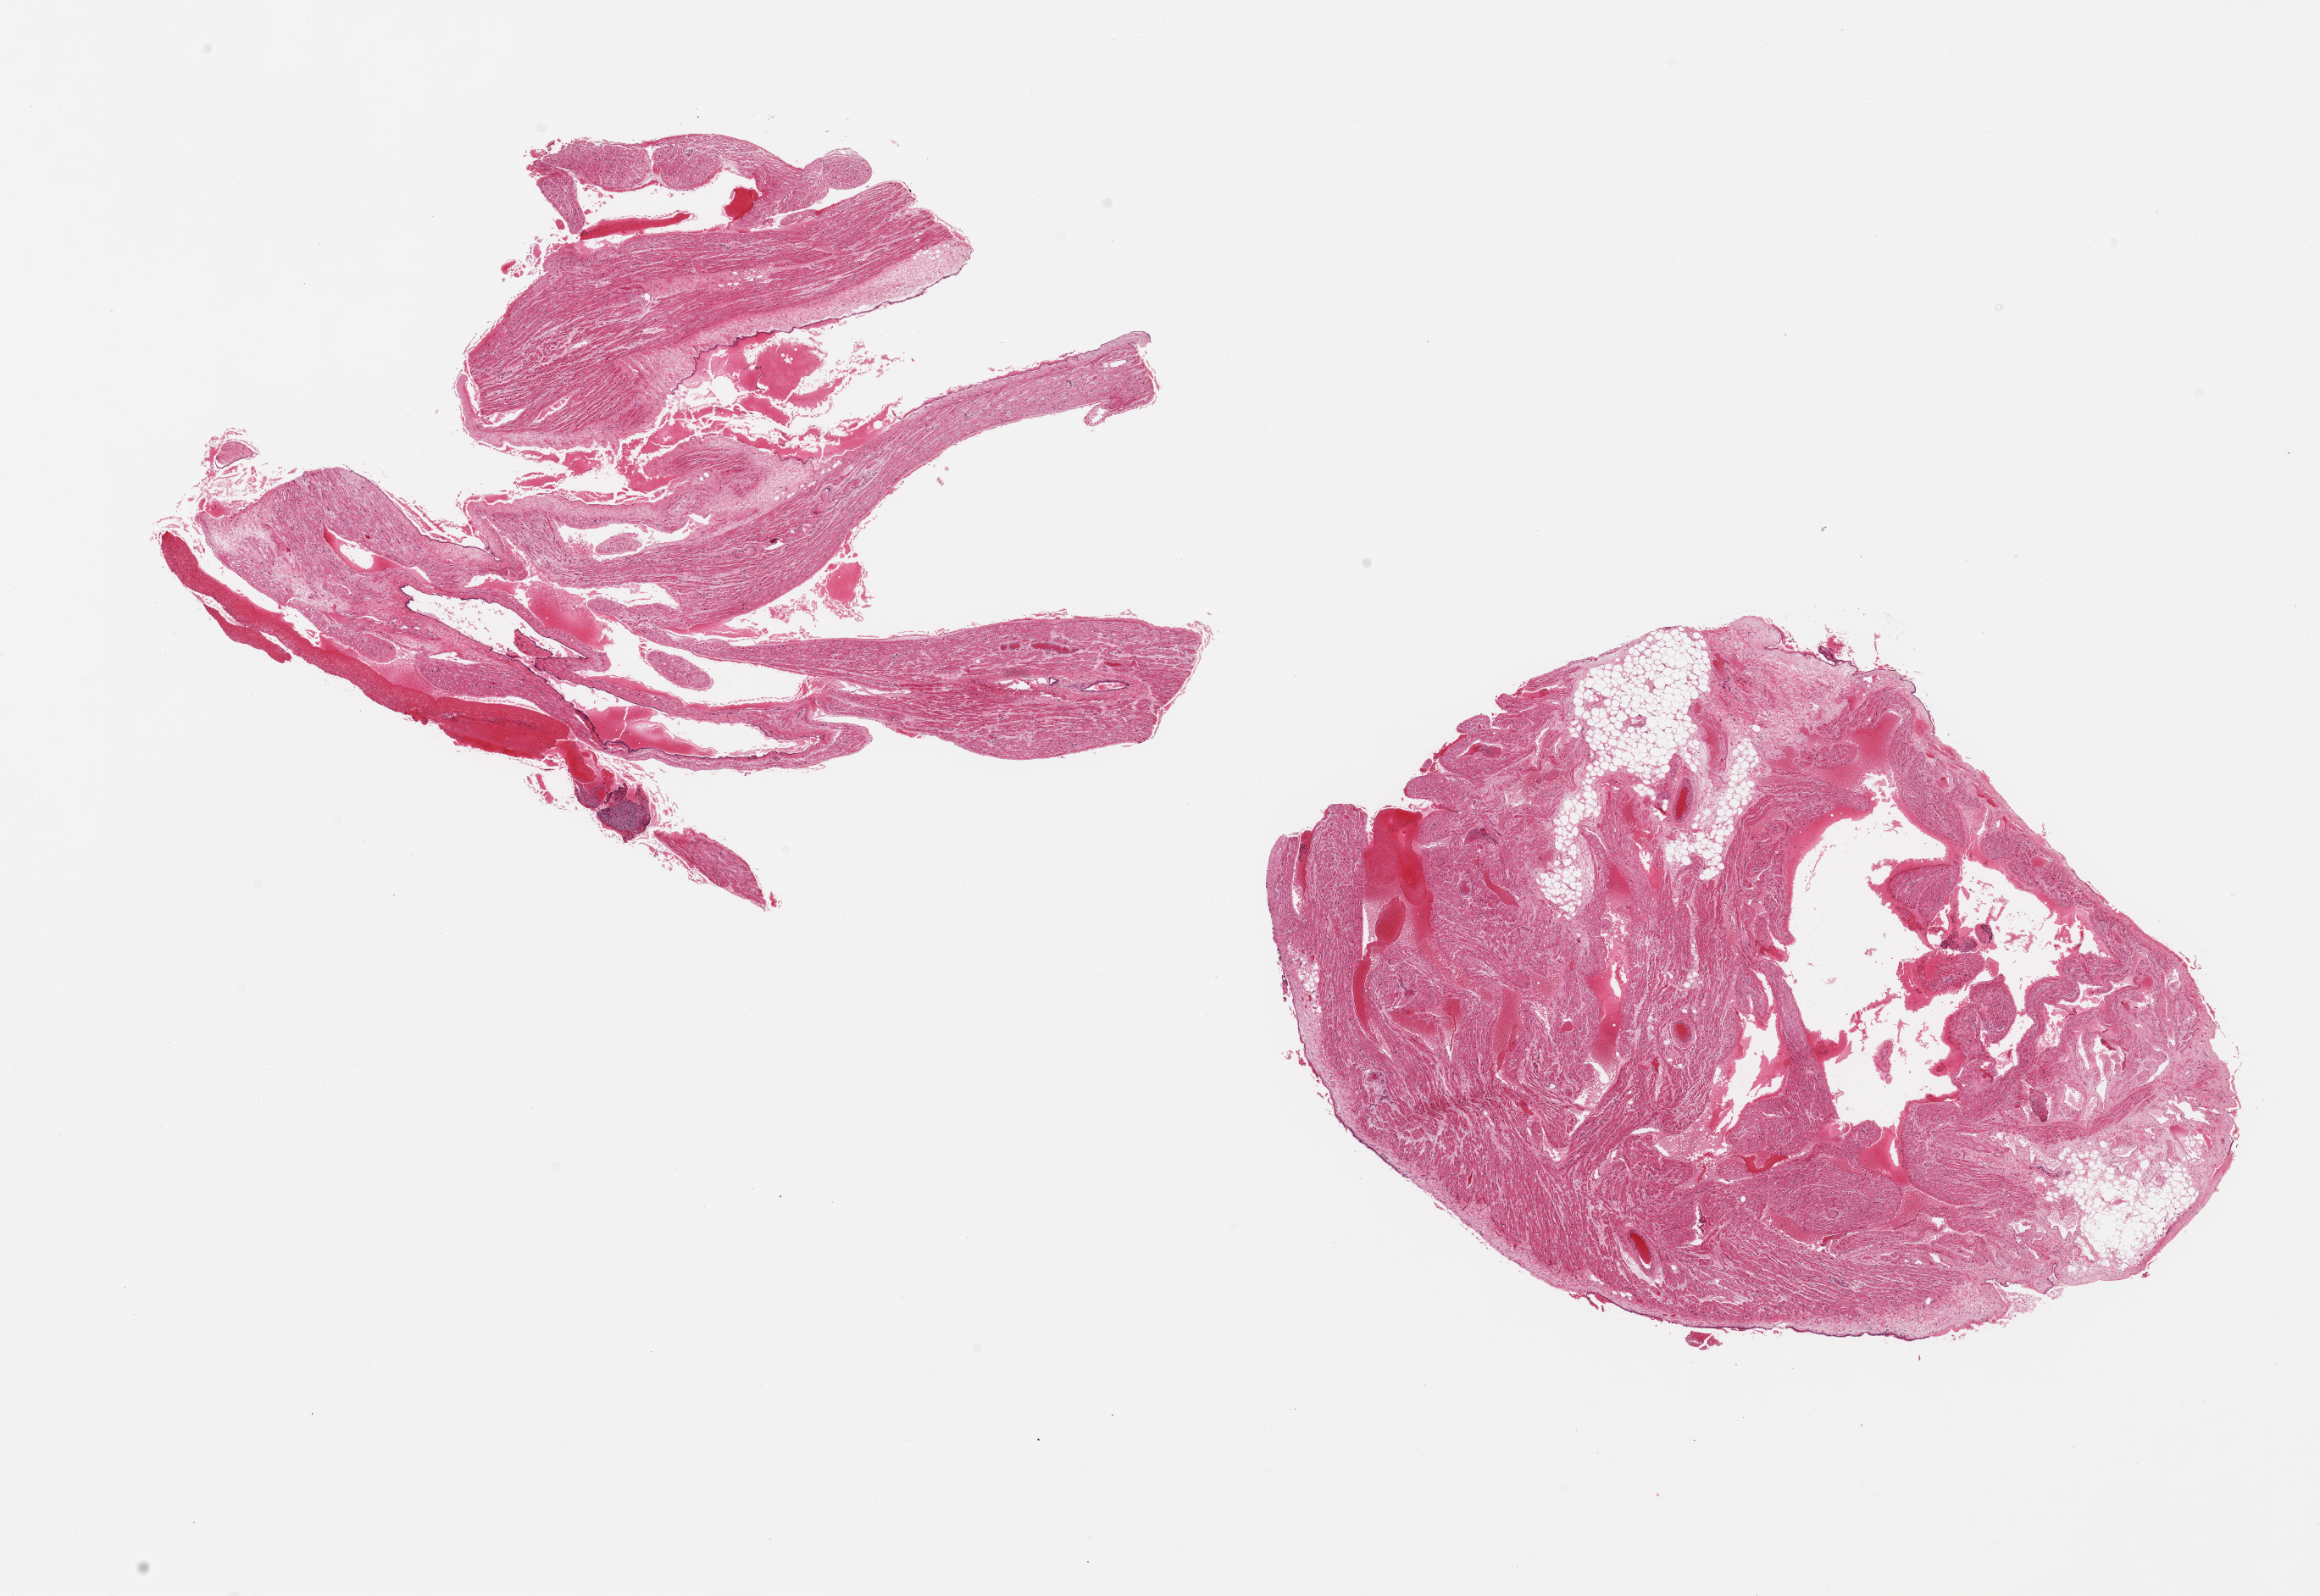
Haematoxylin and eosin whole-slide image — low-resolution overview of the scanned area, about 21.7 x 14.9 mm (from a 20x scan). PAXgene-fixed, paraffin-embedded tissue. Sampled site (target tissue): auricular appendage. Tissue donor sample. Donor: male.
Review note (as recorded): 2 pieces, no abnormalities.